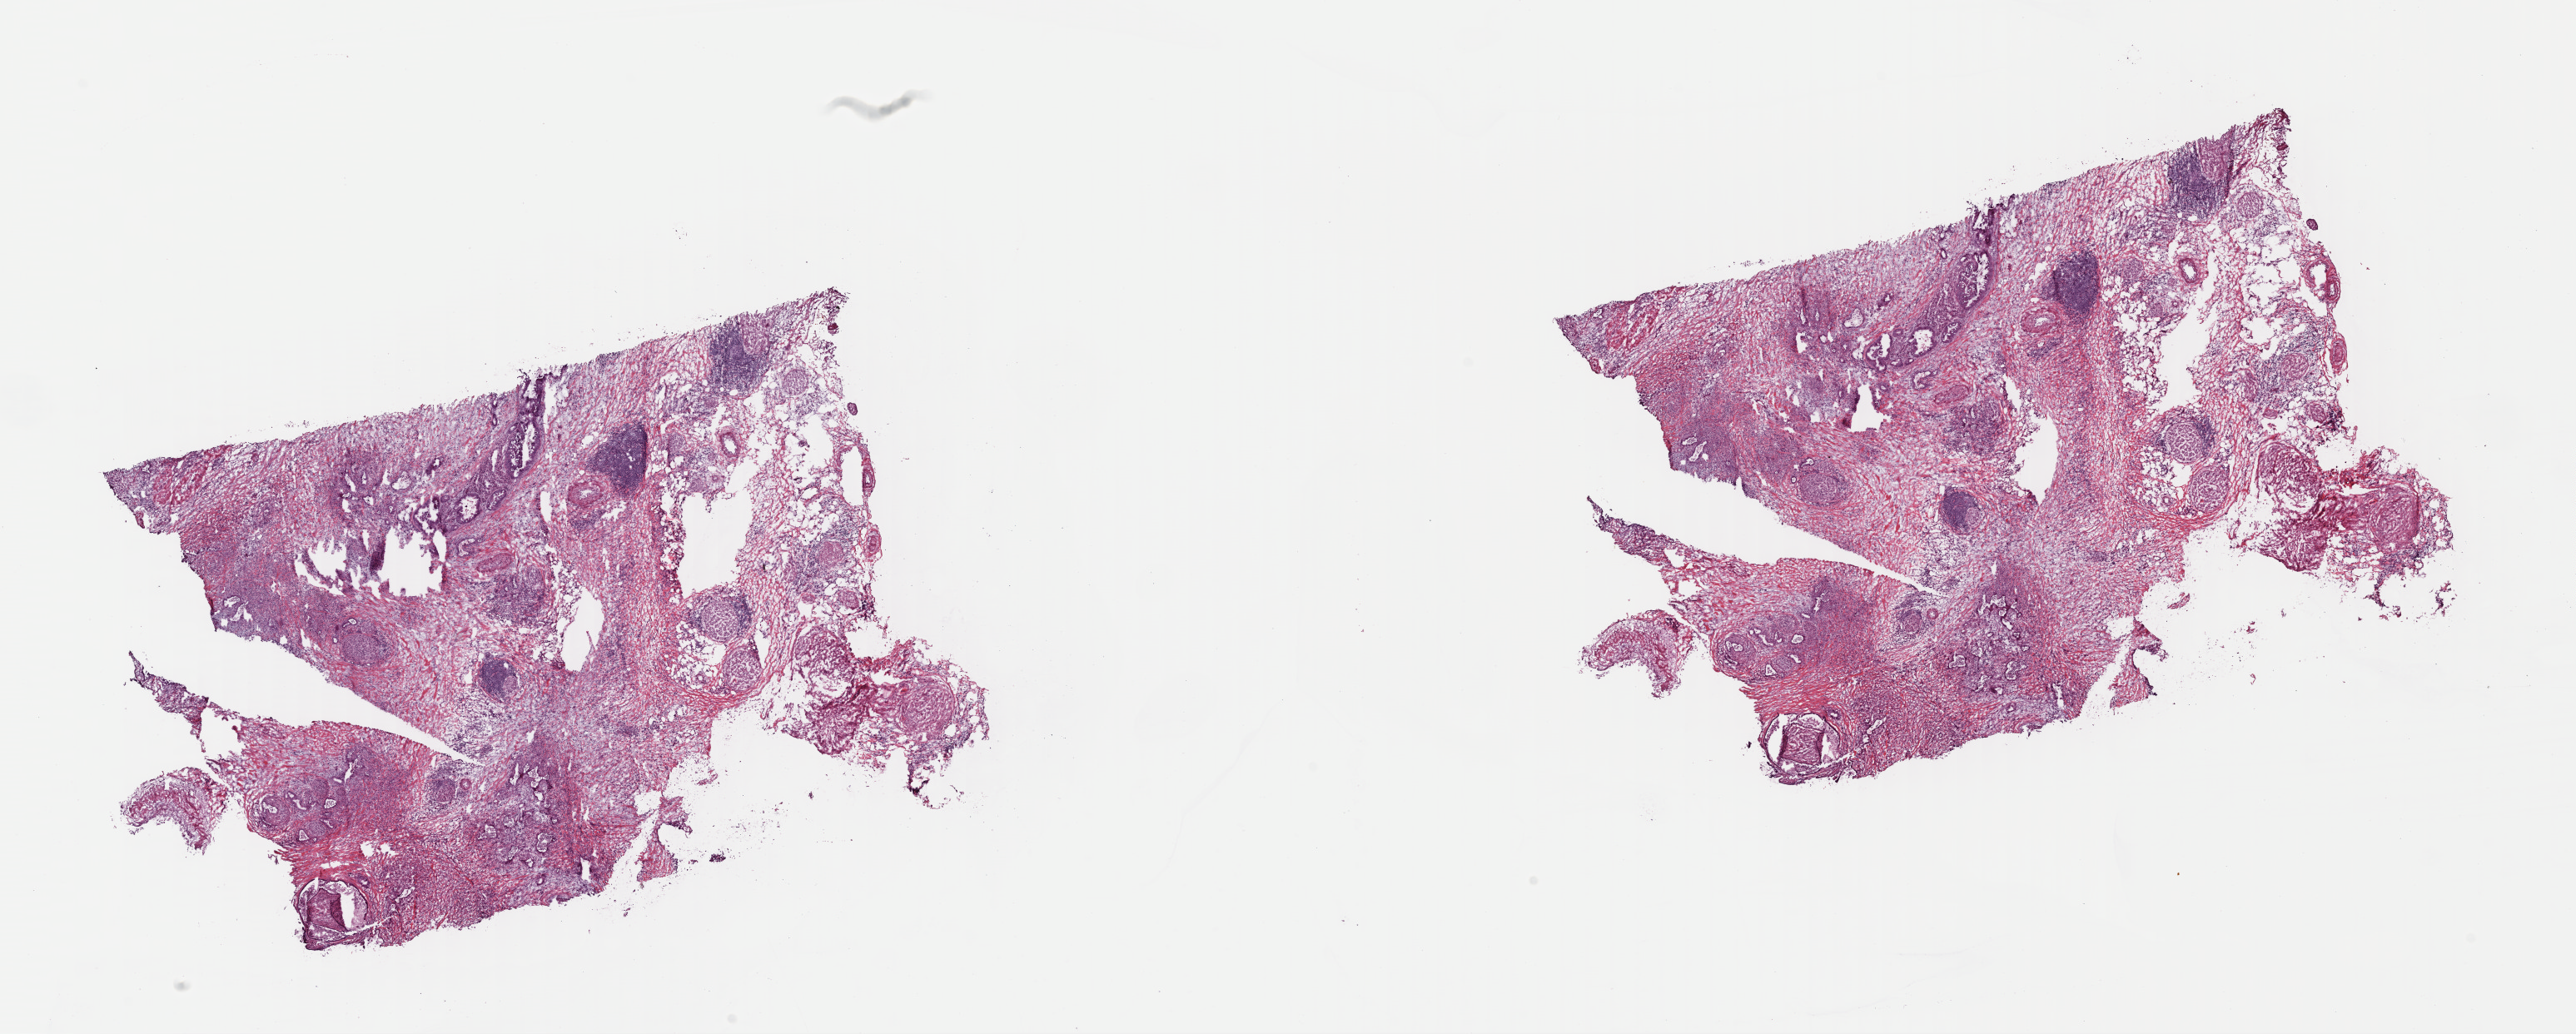
Digitized Hematoxylin and eosin (H&E) stained tissue section (whole slide), low-resolution overview of the scanned area, about 24.3 x 9.8 mm (acquisition: 40x scan), frozen section from the top of the tissue portion, primary tumour sample from the pancreas. Female, age 64 years at initial diagnosis. Histologic grade: G2 (moderately differentiated). Pathologist review of this section (percent, as recorded): tumour cells 18%, tumour nuclei 20%, normal cells 6%, stromal cells 73%, necrosis 3%. Infiltration values recorded for this section: lymphocyte infiltration 15%, monocyte infiltration 2%, neutrophil infiltration 6%.
AJCC pathologic stage: IIB (7th edition). Histologic diagnosis: Infiltrating duct carcinoma, NOS (head of pancreas). TNM: T3 N1 M0. Lymph nodes positive (case pathology): 2 of 16 examined.